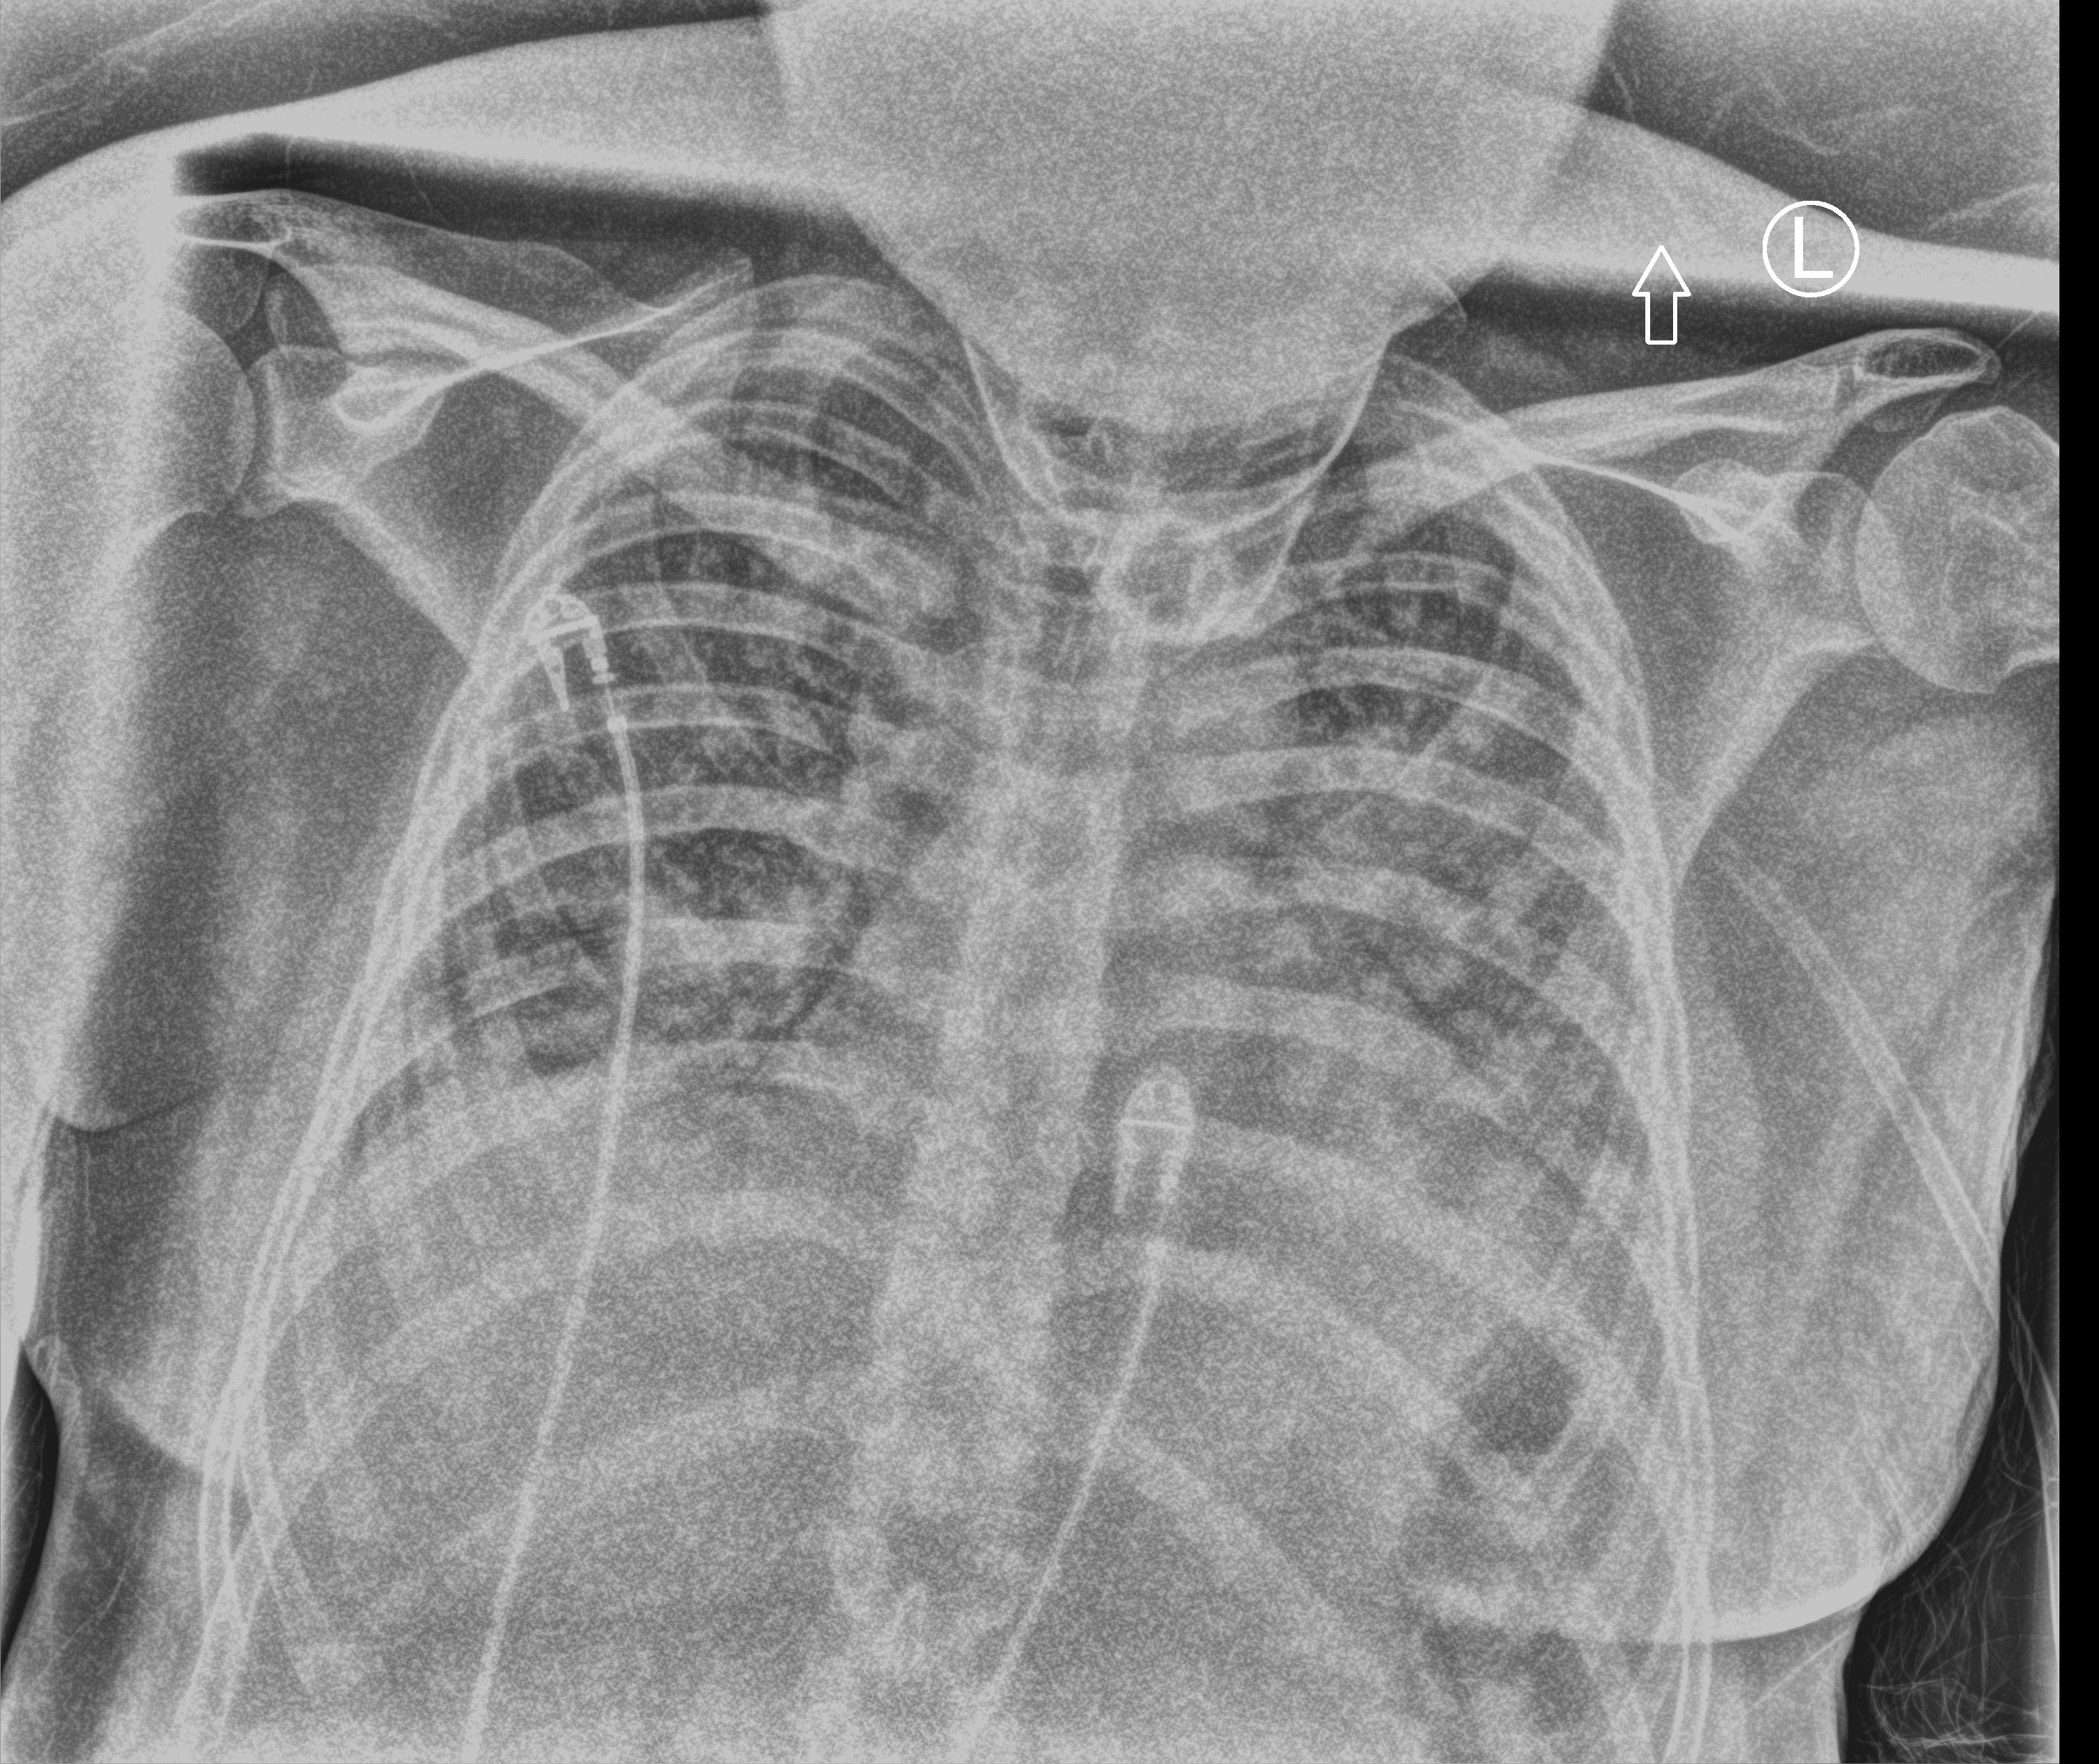
Portable chest radiograph. Male patient hospitalised with COVID-19, age 18–59 years.
From the hospital-stay record, not from the radiograph (when in the stay this image was taken is not recorded): admitted to intensive care during this hospital stay: no; mechanically ventilated during this hospital stay: no.